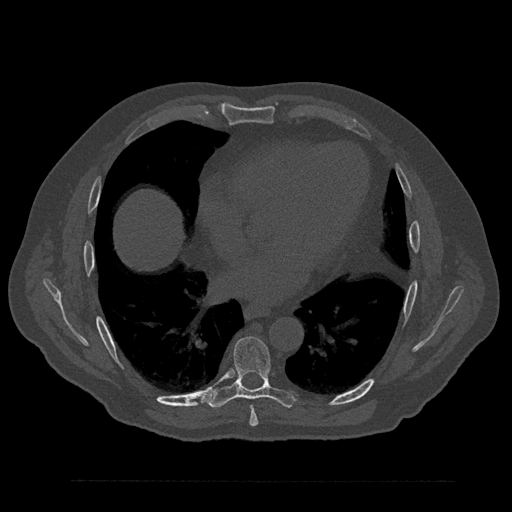
CT including the spine, one axial slice; position 463 of 797 along the scan axis; reconstruction kernel Br40s/3; 120 kVp; bone window (W 1800 / L 400 HU); 512 × 512 image matrix, field of view 430 × 430 mm. Male patient, age 61 years. From the clinical record (not read from this slice): primary cancer: prostate.
Annotated regions visible in this slice (semi-automatically segmented with operator editing):
- T7 vertebra: bounding box [x1, y1, x2, y2] px = [249, 406, 258, 426]
- T8 vertebra: [208, 336, 295, 409]